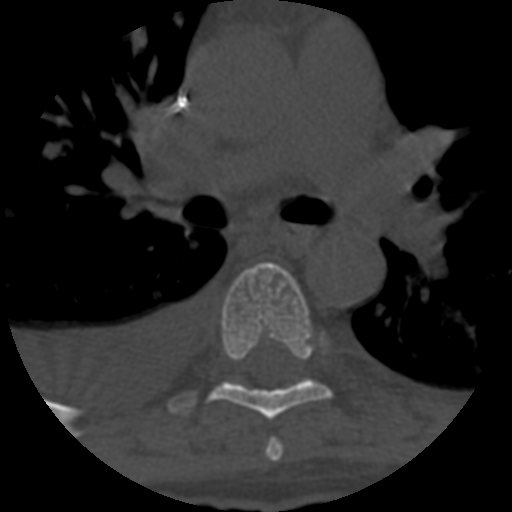
CT including the spine, one axial slice; position 435 of 708 along the scan axis; 120 kVp; one of 3 acquisitions stored at this slice position; bone window (W 1800 / L 400 HU); 1.25 mm slice thickness; 512 × 512 image matrix, field of view 160 × 160 mm. Patient age 55 years. From the clinical record (not read from this slice): primary cancer: colon; vertebrae with lytic lesions (as recorded): T12, L1, L5.
Outlined on this slice (semi-automatically segmented with operator editing):
- T5 vertebra: bounding box [x1, y1, x2, y2] px = [266, 440, 282, 462]
- T6 vertebra: [211, 262, 331, 421]